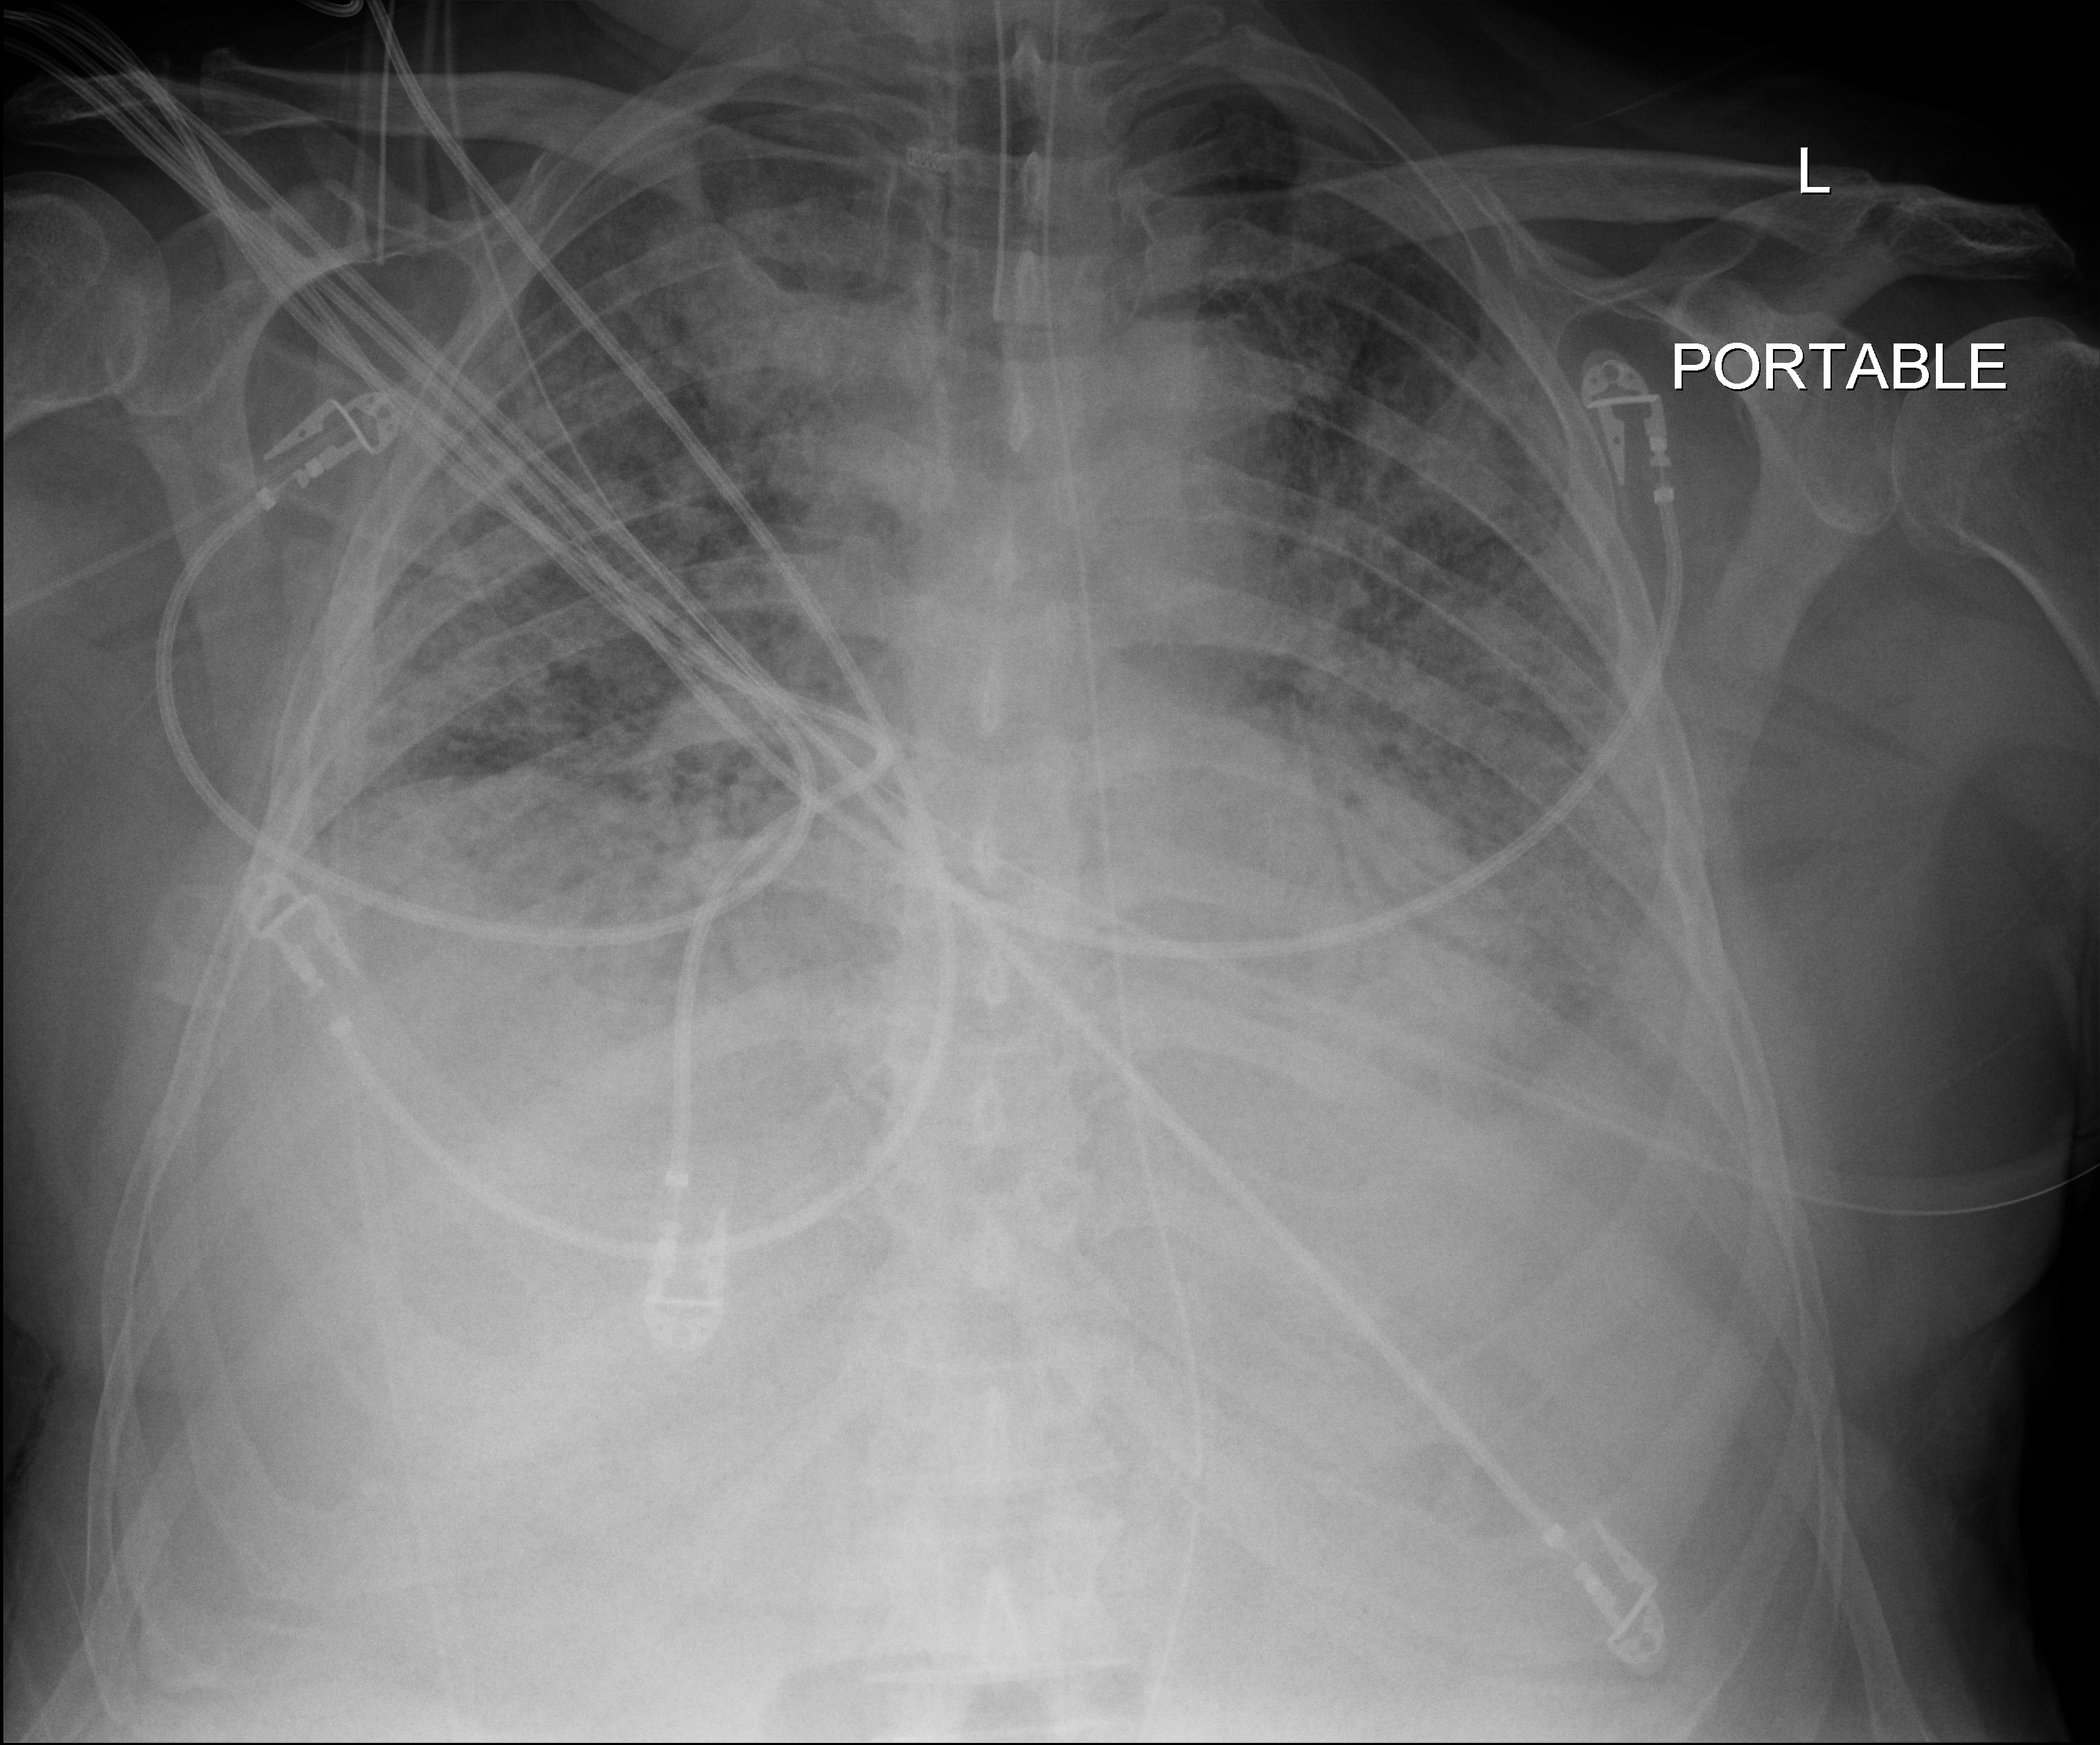
Chest X-ray (portable); anteroposterior (AP) projection. Male patient hospitalised with COVID-19, age 60–74 years.
Hospital-stay facts (about this admission, not read from this image; timing relative to this image not recorded):
- mechanically ventilated during this hospital stay: yes